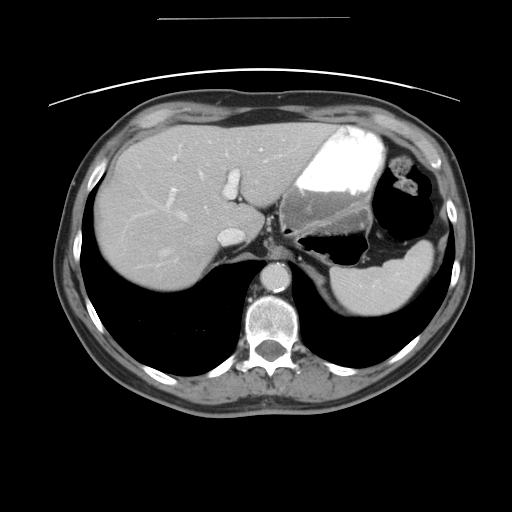
Contrast-enhanced abdominal CT, one axial slice. Slice 35 of 49 in the series (ordered by position). Intravenous contrast given. Soft-tissue window (W 400 / L 40 HU). 5 mm slice thickness. 512 × 512 image matrix, field of view 413 × 413 mm. Male patient, age 57 years. Case-level facts recorded for this patient, not image findings: diagnosis: colorectal cancer liver metastases, imaged before liver resection; multiple liver metastases: yes; largest metastasis: 4 cm; disease in both lobes: no.
Outlined on this slice (outlined manually by an expert reader):
- hepatic veins: bounding box <161,158,266,254> (left, top, right, bottom; pixels)
- liver: <96,122,336,290>
- planned liver remnant (the part of the liver to remain after resection): <208,122,335,236>
- portal vein (with intrahepatic branches): <141,139,262,214>